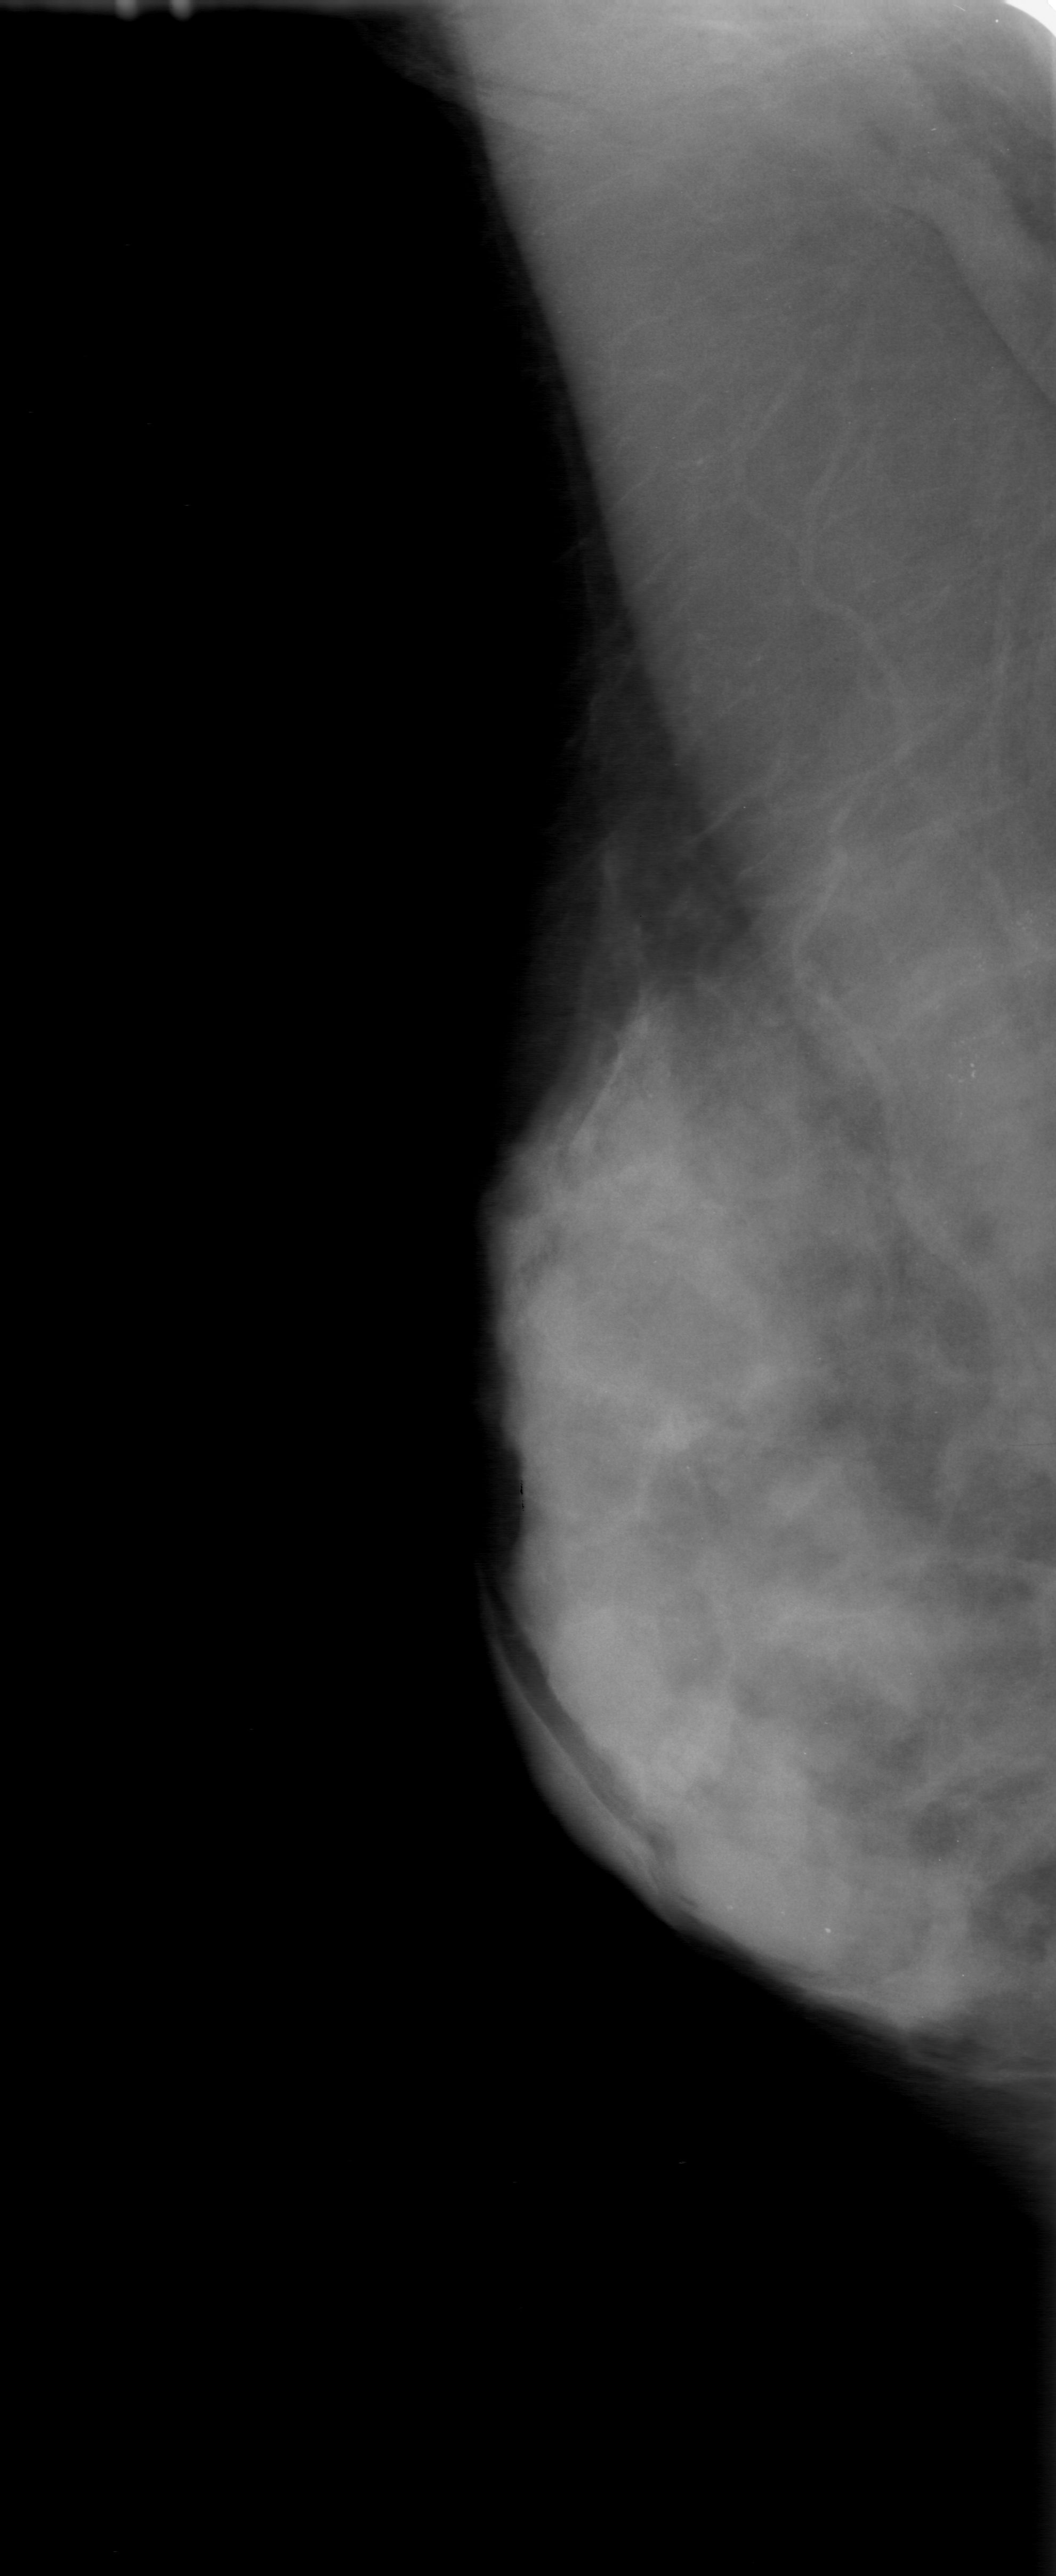
Mammogram (digitized film); right breast; mediolateral oblique (MLO) view; BI-RADS breast density category 4 (scale 1–4).
Abnormality record for this image: calcifications, morphology pleomorphic, distribution clustered; BI-RADS assessment category 0; pathology (as recorded): malignant.